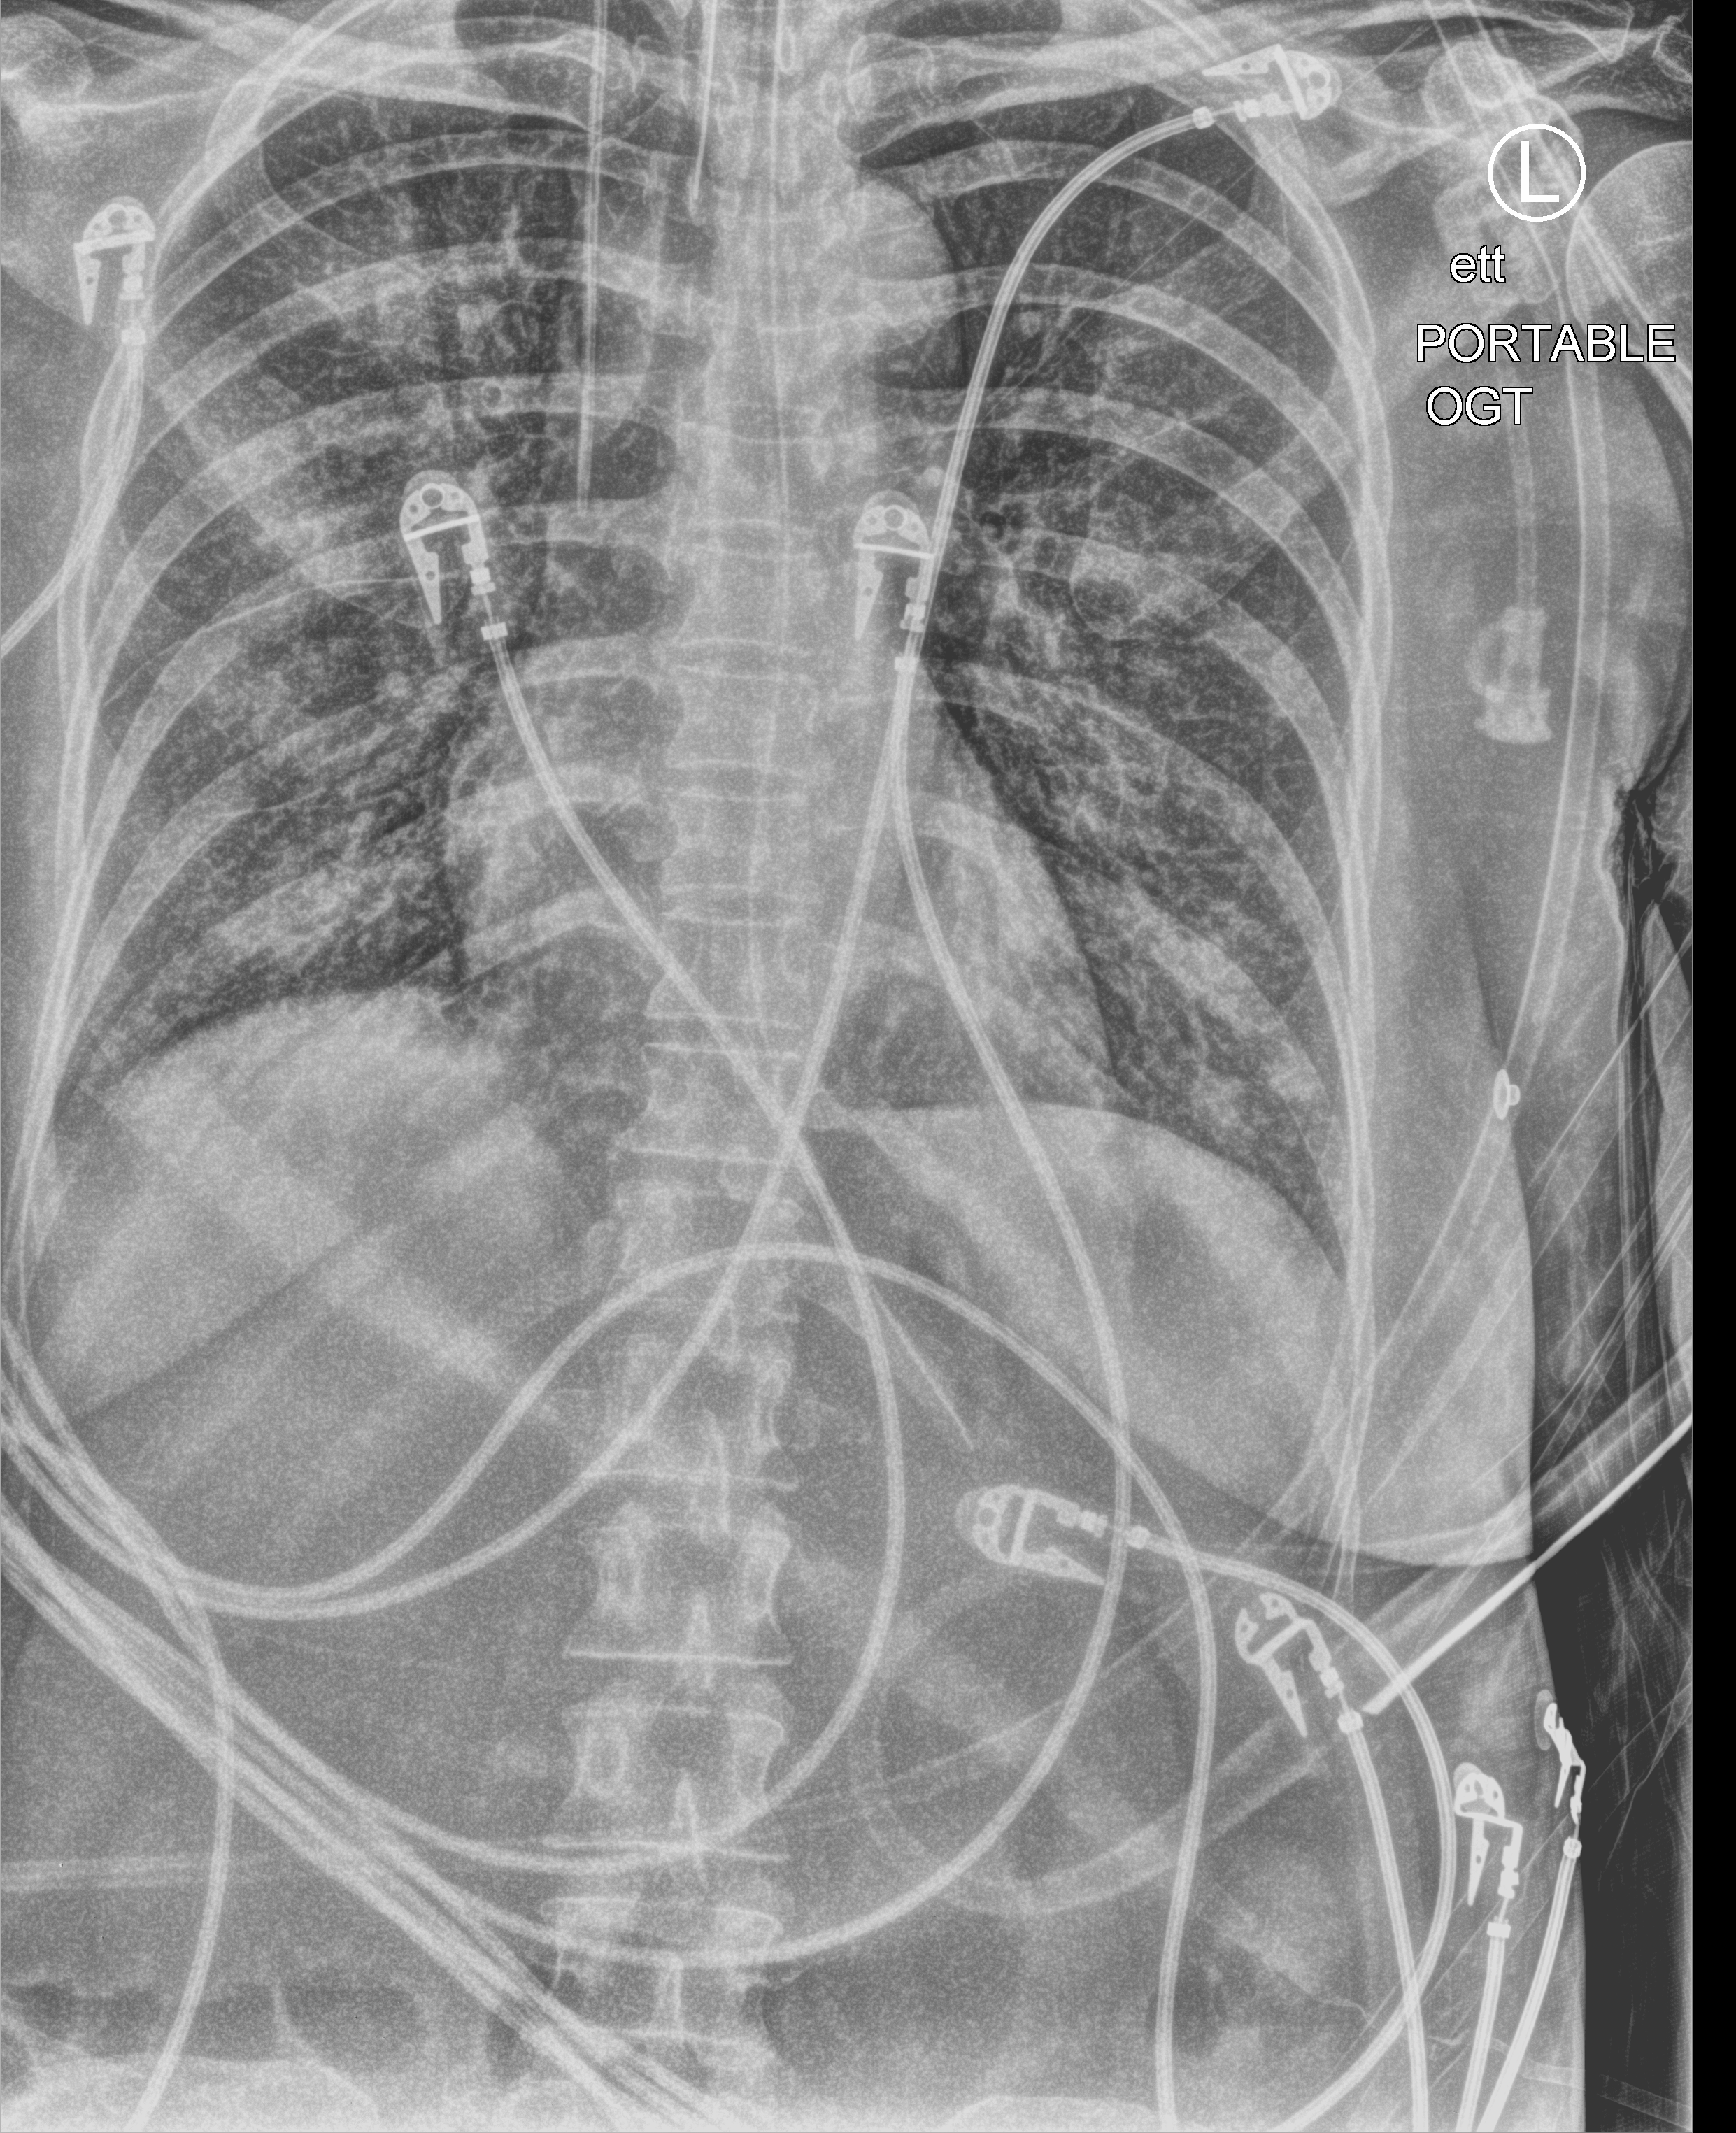
Chest X-ray (portable). Female patient hospitalised with COVID-19, age 18–59 years.
From the hospital-stay record, not from the radiograph (when in the stay this image was taken is not recorded): mechanically ventilated during this hospital stay: yes; admitted to intensive care during this hospital stay: yes; other chronic lung disease (admission record): no.